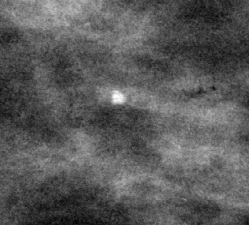
Region of interest cut from a scanned film mammogram (one marked finding), left breast, CC view, BI-RADS breast density category 2 (scale 1–4).
Finding: calcifications, morphology punctate; BI-RADS assessment category 2; benign without callback (not worked up further).